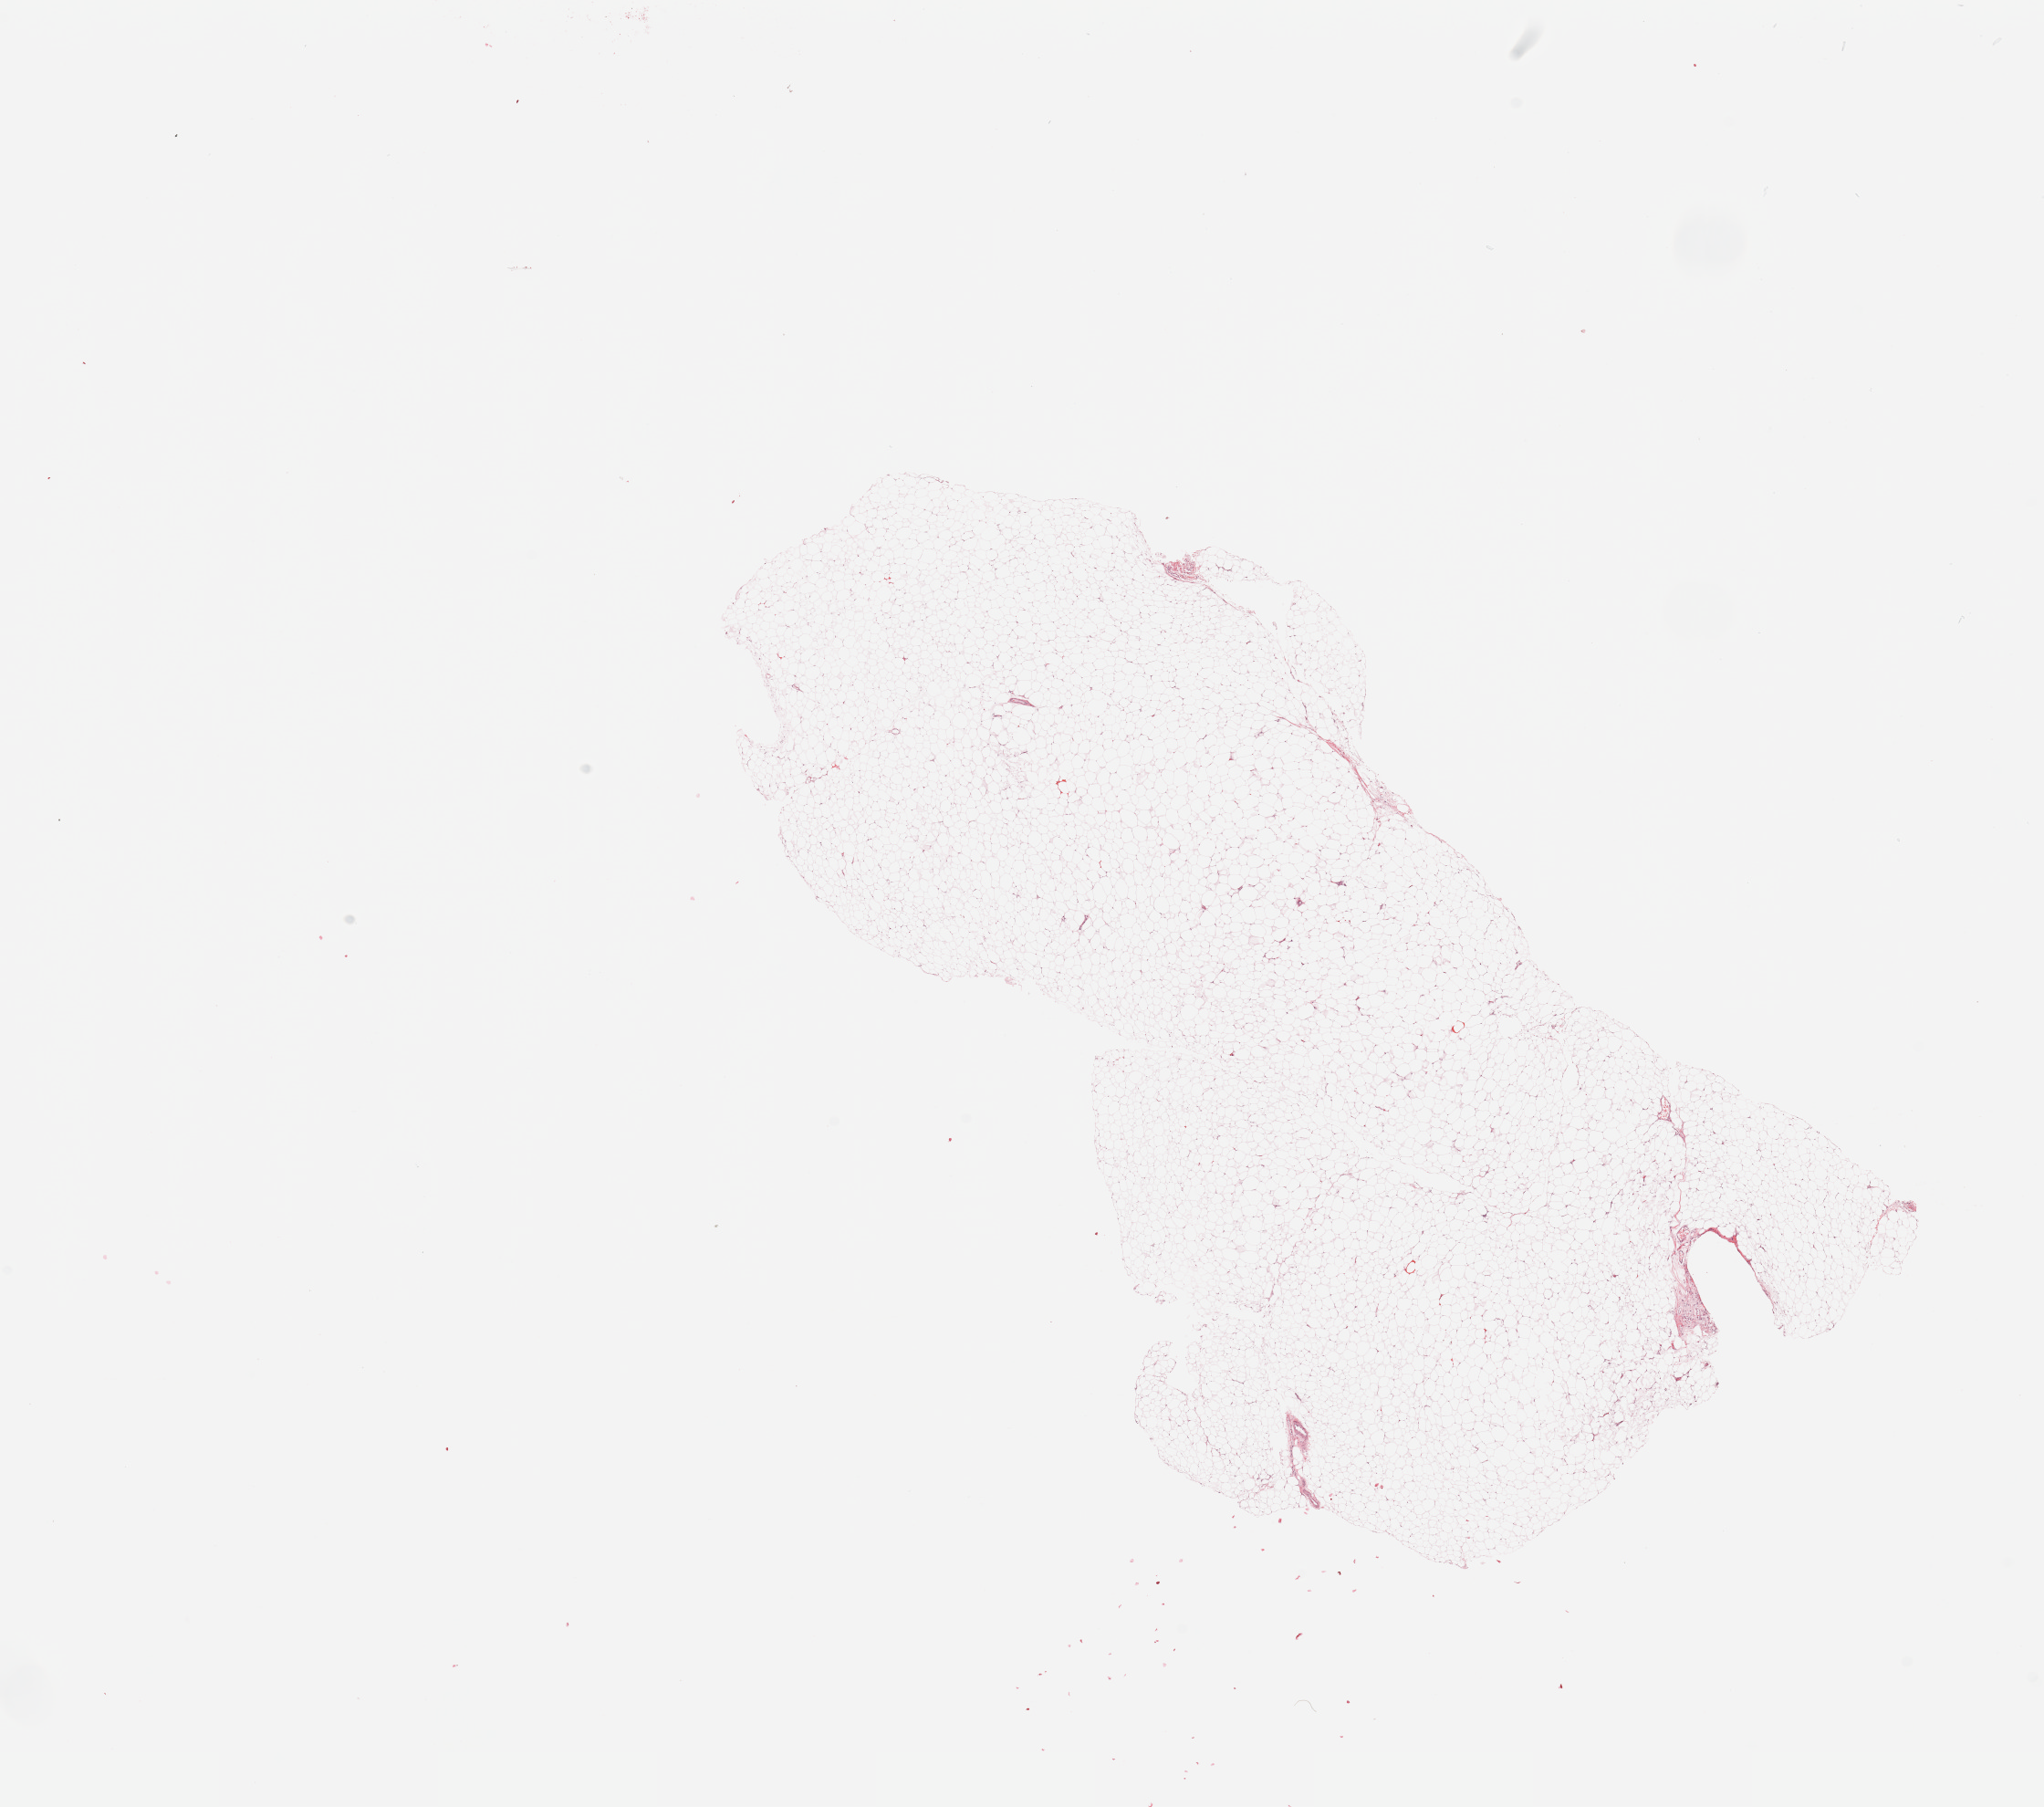
Hematoxylin and eosin (H&E) stained whole-slide image, shown as a low-resolution overview of the whole scanned area (about 17.7 x 15.7 mm, acquisition: 20x scan). Normal (non-tumour) tissue sample, kidney. 57-year-old female patient.
This section: normal (non-tumour) tissue from the same patient. Patient diagnosis: Renal cell carcinoma, NOS.